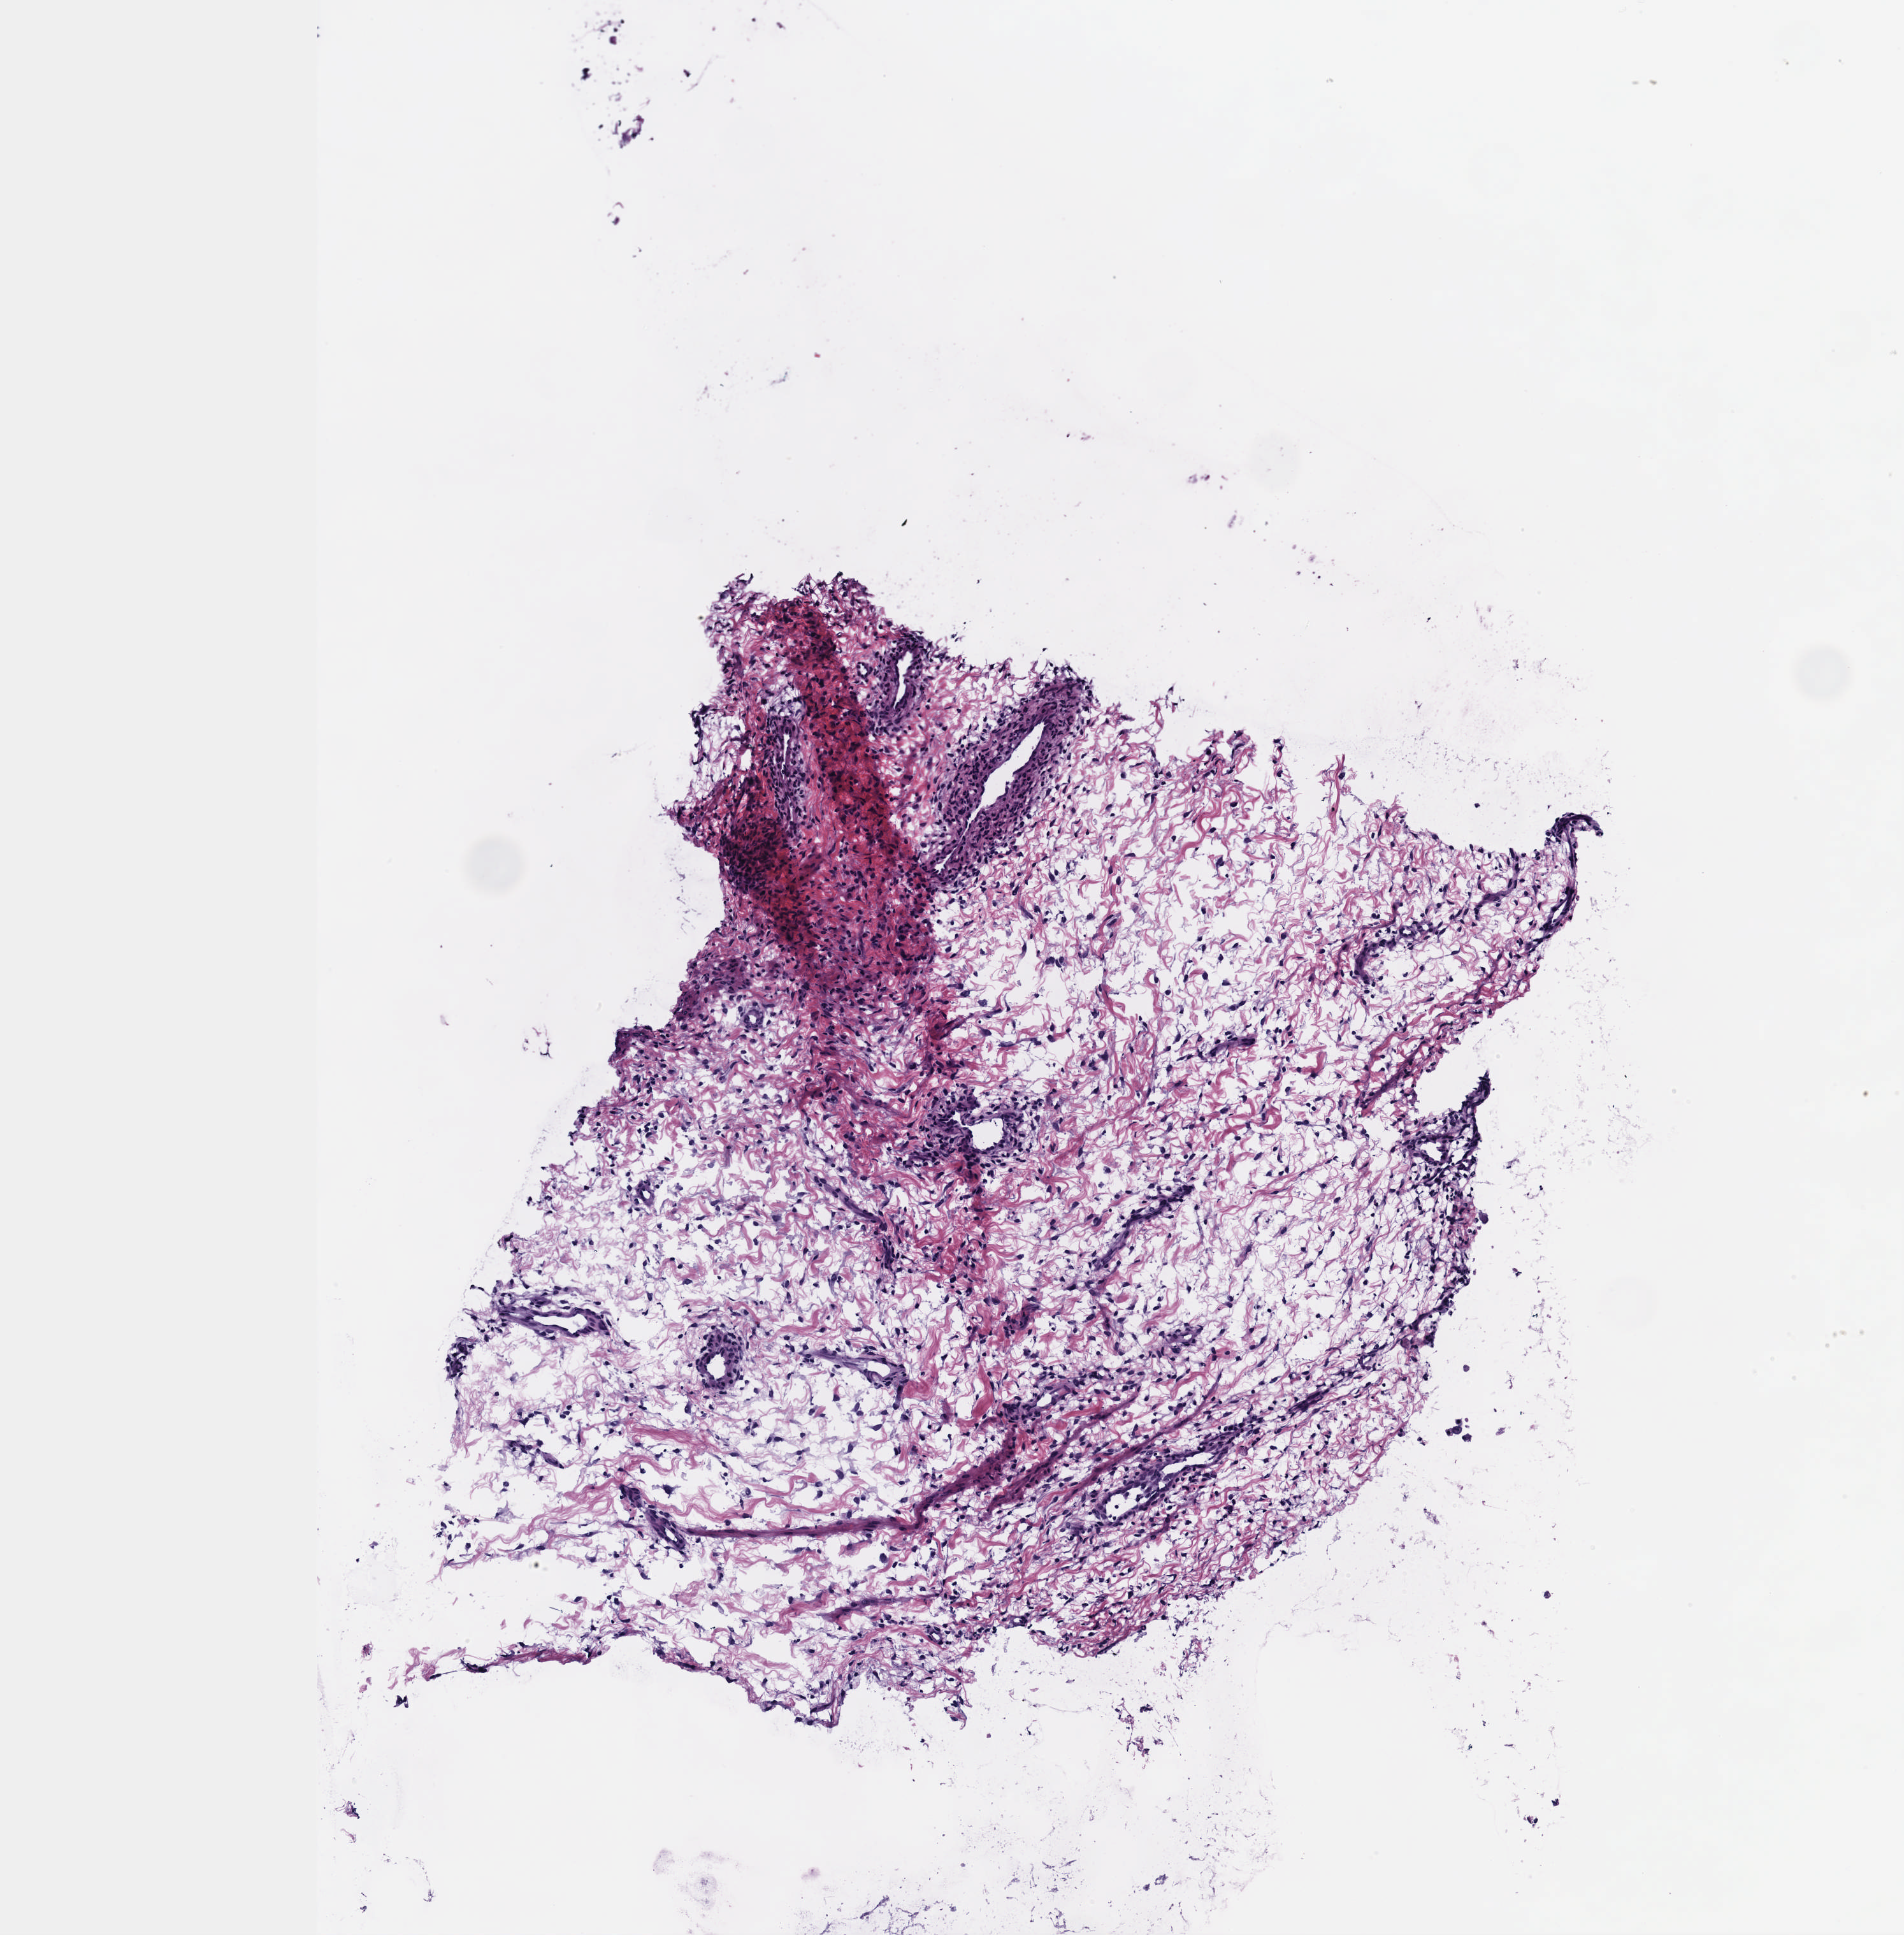
Whole-slide histology image, H&E — a low-resolution overview of the entire scanned area, about 3.0 x 3.1 mm. Male patient.
Specimen: frozen section from the top of the tissue portion; testis, primary tumour sample.